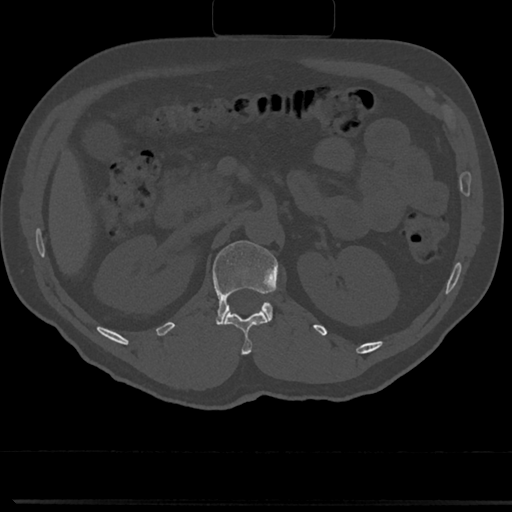
CT including the spine, one axial slice; position 107 of 817 along the scan axis; 120 kVp; bone window (W 1800 / L 400 HU); 0.5 mm slice thickness; 512 × 512 image matrix, field of view 355 × 355 mm. Patient: male, 61 years. From the clinical record (not read from this slice): primary cancer: prostate.
Outlined on this slice (semi-automatic segmentation, software-assisted and operator-edited):
- L1 vertebra: bounding box <194,240,278,326> (left, top, right, bottom; pixels)
- T12 vertebra: <224,311,268,353>